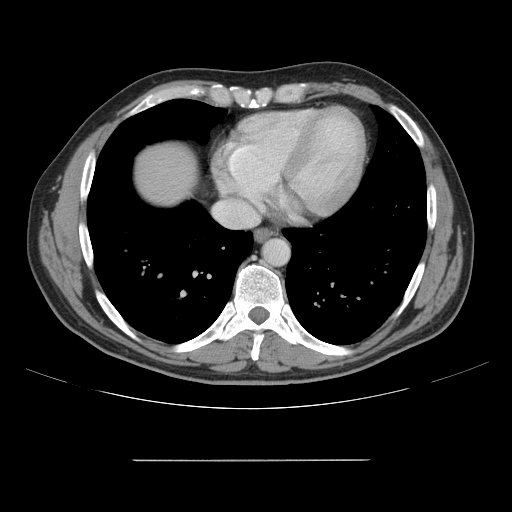
Contrast-enhanced abdominal CT, one axial slice; slice 149 of 164 in the series (ordered by position); 120 kVp; intravenous contrast given; soft-tissue window (W 400 / L 40 HU); 512 × 512 image matrix, field of view 404 × 404 mm. Male patient, age 54 years. From the clinical record (not read from this slice): diagnosis: colorectal cancer liver metastases, imaged before liver resection; multiple liver metastases: yes; largest metastasis: 1 cm; disease in both lobes: no.
Outlined on this slice (outlined manually by an expert reader):
- hepatic veins: bounding box <214,201,258,226> (left, top, right, bottom; pixels)
- liver: <134,144,195,203>
- planned liver remnant (the part of the liver to remain after resection): <134,144,194,203>